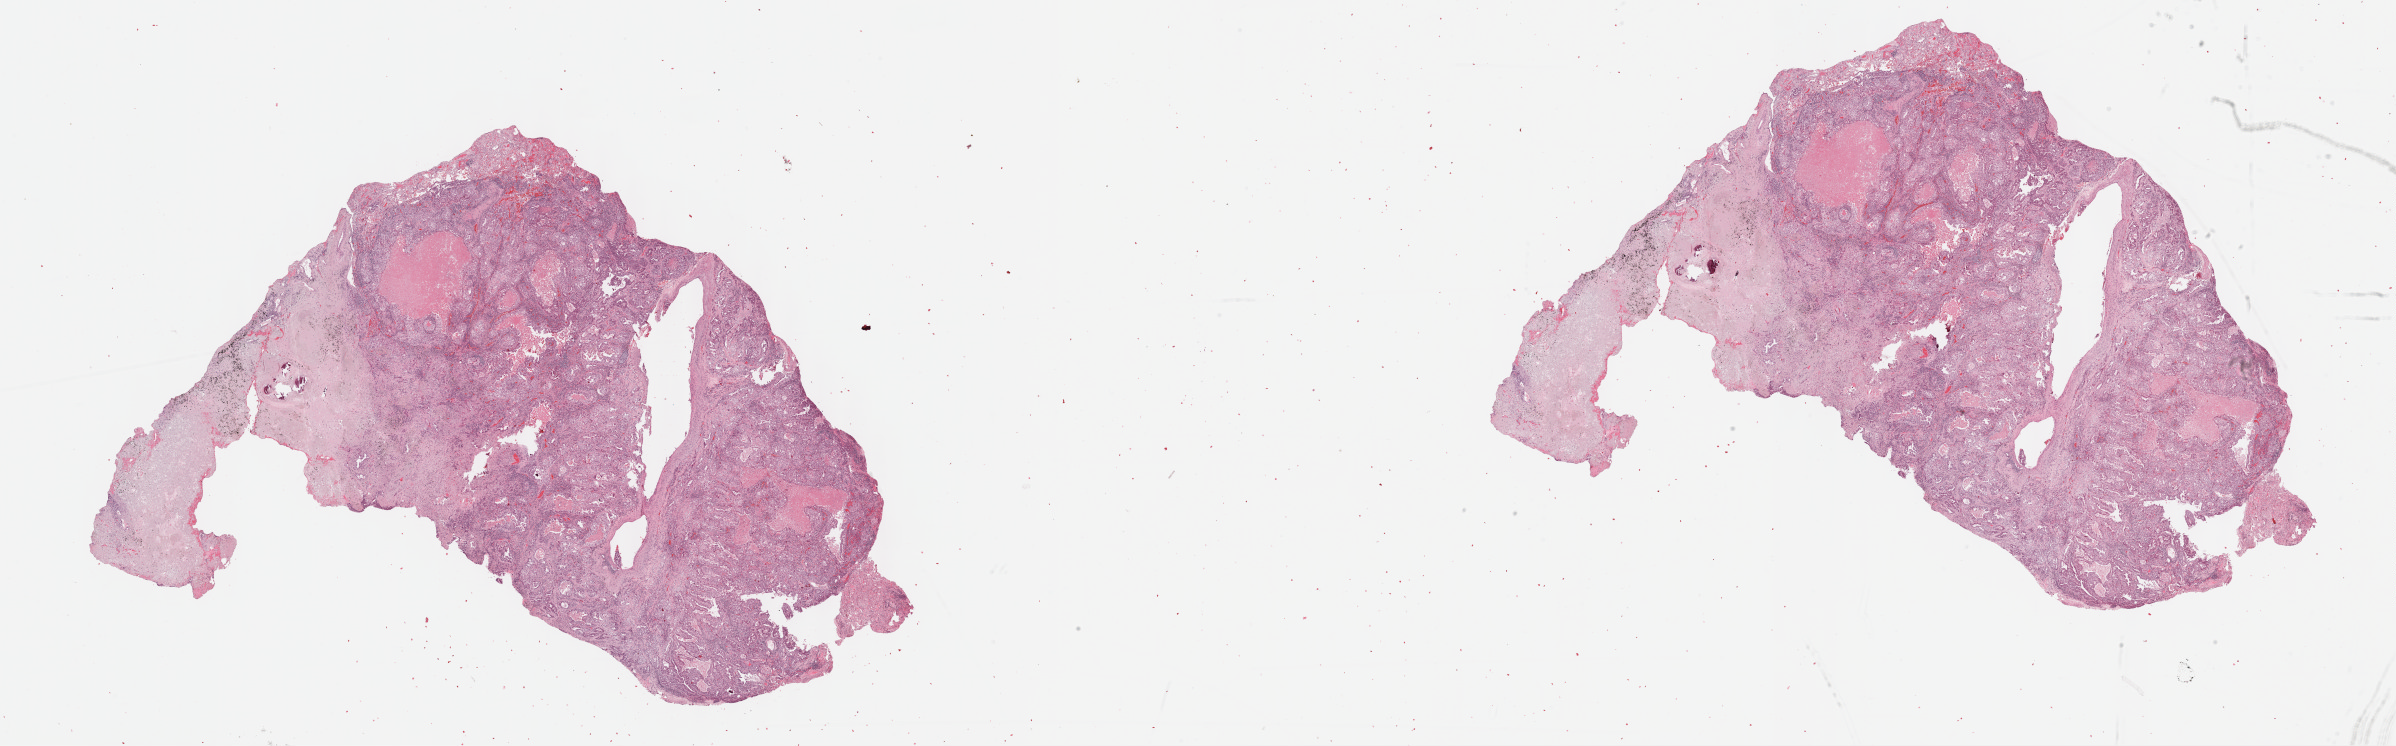
Whole-slide histology image, H&E-stained, shown as a low-resolution overview of the whole scanned area (about 38.8 x 12.1 mm, from a 40x scan), formalin-fixed paraffin-embedded (FFPE) diagnostic section, lung, primary tumour sample. Female patient; age at initial diagnosis 77 years.
Pathologic diagnosis: Adenocarcinoma, NOS (upper lobe, lung). AJCC pathologic stage: IA (6th edition).